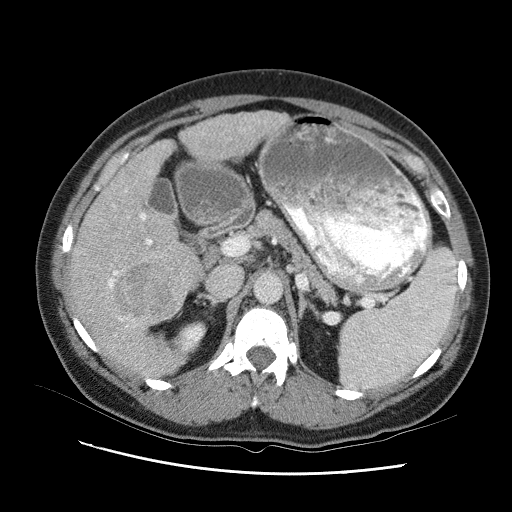
Contrast-enhanced abdominal CT (liver protocol), one axial slice. Slice 53 of 95 in the series (ordered by position). Reconstruction kernel STANDARD. 120 kVp. One of 2 acquisitions stored at this slice position. Soft-tissue window (W 400 / L 40 HU). 512 × 512 image matrix. From the clinical record (not read from this slice): diagnosis: hepatocellular carcinoma (patient treated with transarterial chemoembolisation; whether this scan precedes or follows treatment is not stated here); TNM stage (as recorded): Stage-I; Child-Pugh class: B; tumour nodularity: uninodular.
Structures marked on this image (semi-automatically segmented with operator editing):
- liver parenchyma outside the tumour (the mass and vessels are separate outlines, so this box may not span the whole liver): bounding box [x1, y1, x2, y2] px = [66, 104, 292, 374]
- mass: [120, 255, 179, 318]
- liver vessels: [99, 124, 244, 337]